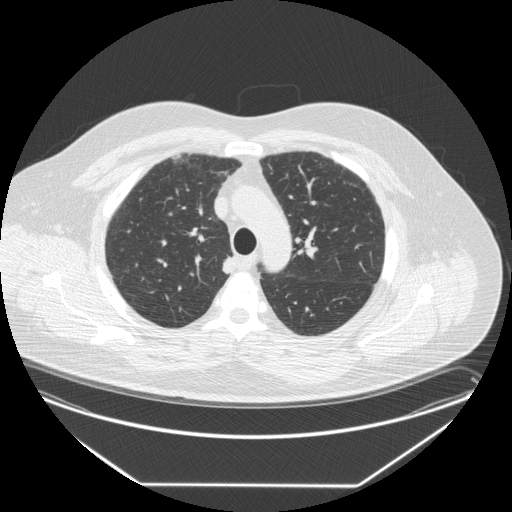
Axial slice from a low-dose chest CT screening exam; third annual screen; lung window (W 1500 / L -600 HU); 2.5 mm slice thickness; standard (soft-tissue) reconstruction kernel (STANDARD); slice 58 of 258 in the series. Male participant, aged 58 years at enrolment. Former smoker at enrolment.
- Expert reader's lesion annotation, box from (x=214, y=252) to (x=246, y=282) px.
- Screening reader's record for this exam (one nodule recorded; not confirmed to be the boxed lesion): non-calcified nodule or mass ≥4 mm, right upper lobe, 15 × 12 mm, smooth margins, soft tissue attenuation, pre-existing on the prior screen: no.
- Later outcome: lung cancer diagnosed 17 days after this screen — large cell carcinoma, NOS, right upper lobe, stage IV (AJCC 6th edition), 35 mm at pathology.